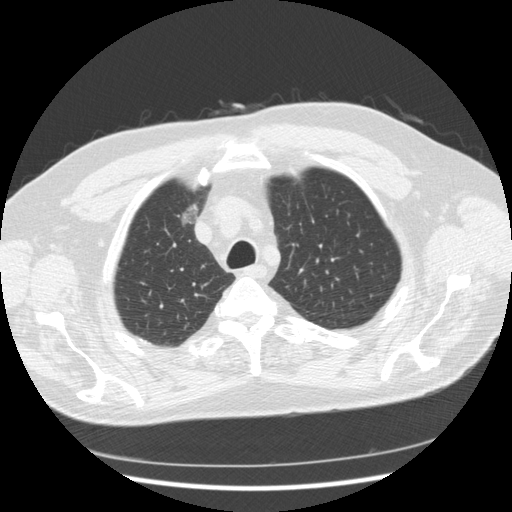
Axial slice from a low-dose chest CT screening exam, second screening round (one year after baseline), lung window (W 1500 / L -600 HU), 2.5 mm slice thickness, standard (soft-tissue) reconstruction kernel (STANDARD), slice 45 of 267 in the series. Male, age 66 years at enrolment. Former smoker at enrolment.
Expert-annotated lung lesion, bounding box [x1, y1, x2, y2] px = [158, 198, 211, 240]. Screening reader's record for this exam: no non-calcified nodule ≥4 mm recorded.